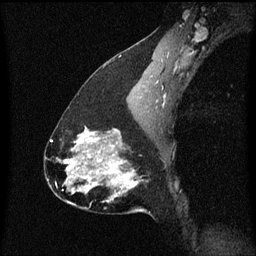
Breast MRI (dynamic contrast-enhanced), one sagittal slice. Slice 36 of 60 in the series (ordered by position). Dynamic contrast-enhanced series, image 2 of 3 at this slice position (ordered by acquisition). 1.5 T. TE 4.2 ms, TR 8.4 ms. 2 mm slice thickness. 256 × 256 image matrix. Patient: female, 47 years.
Structures marked on this image (semi-automatic segmentation, software-assisted and operator-edited):
- analysis volume of interest (the breast-tissue region the enhancement analysis was run in; not a lesion): bounding box [x1, y1, x2, y2] px = [81, 138, 147, 213]
- tumour enhancement mask (voxels above the 70 % enhancement threshold inside the analysis volume of interest): [81, 138, 137, 195]